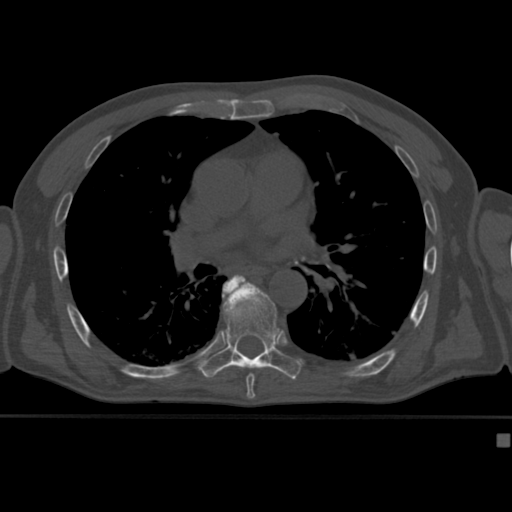
CT including the spine, one axial slice. Slice 268 of 430 in the series (ordered by position). 120 kVp. Bone window (W 1800 / L 400 HU). 1.5 mm slice thickness. 512 × 512 image matrix, field of view 337 × 337 mm. Patient: male, 64 years. From the clinical record (not read from this slice): primary cancer: uterus; vertebrae with lytic lesions (as recorded): T1, T4, T5, T7, L5.
Structures marked on this image (semi-automatic segmentation, software-assisted and operator-edited):
- T7 vertebra: bounding box [x1, y1, x2, y2] px = [242, 278, 255, 382]
- T8 vertebra: [200, 275, 302, 382]